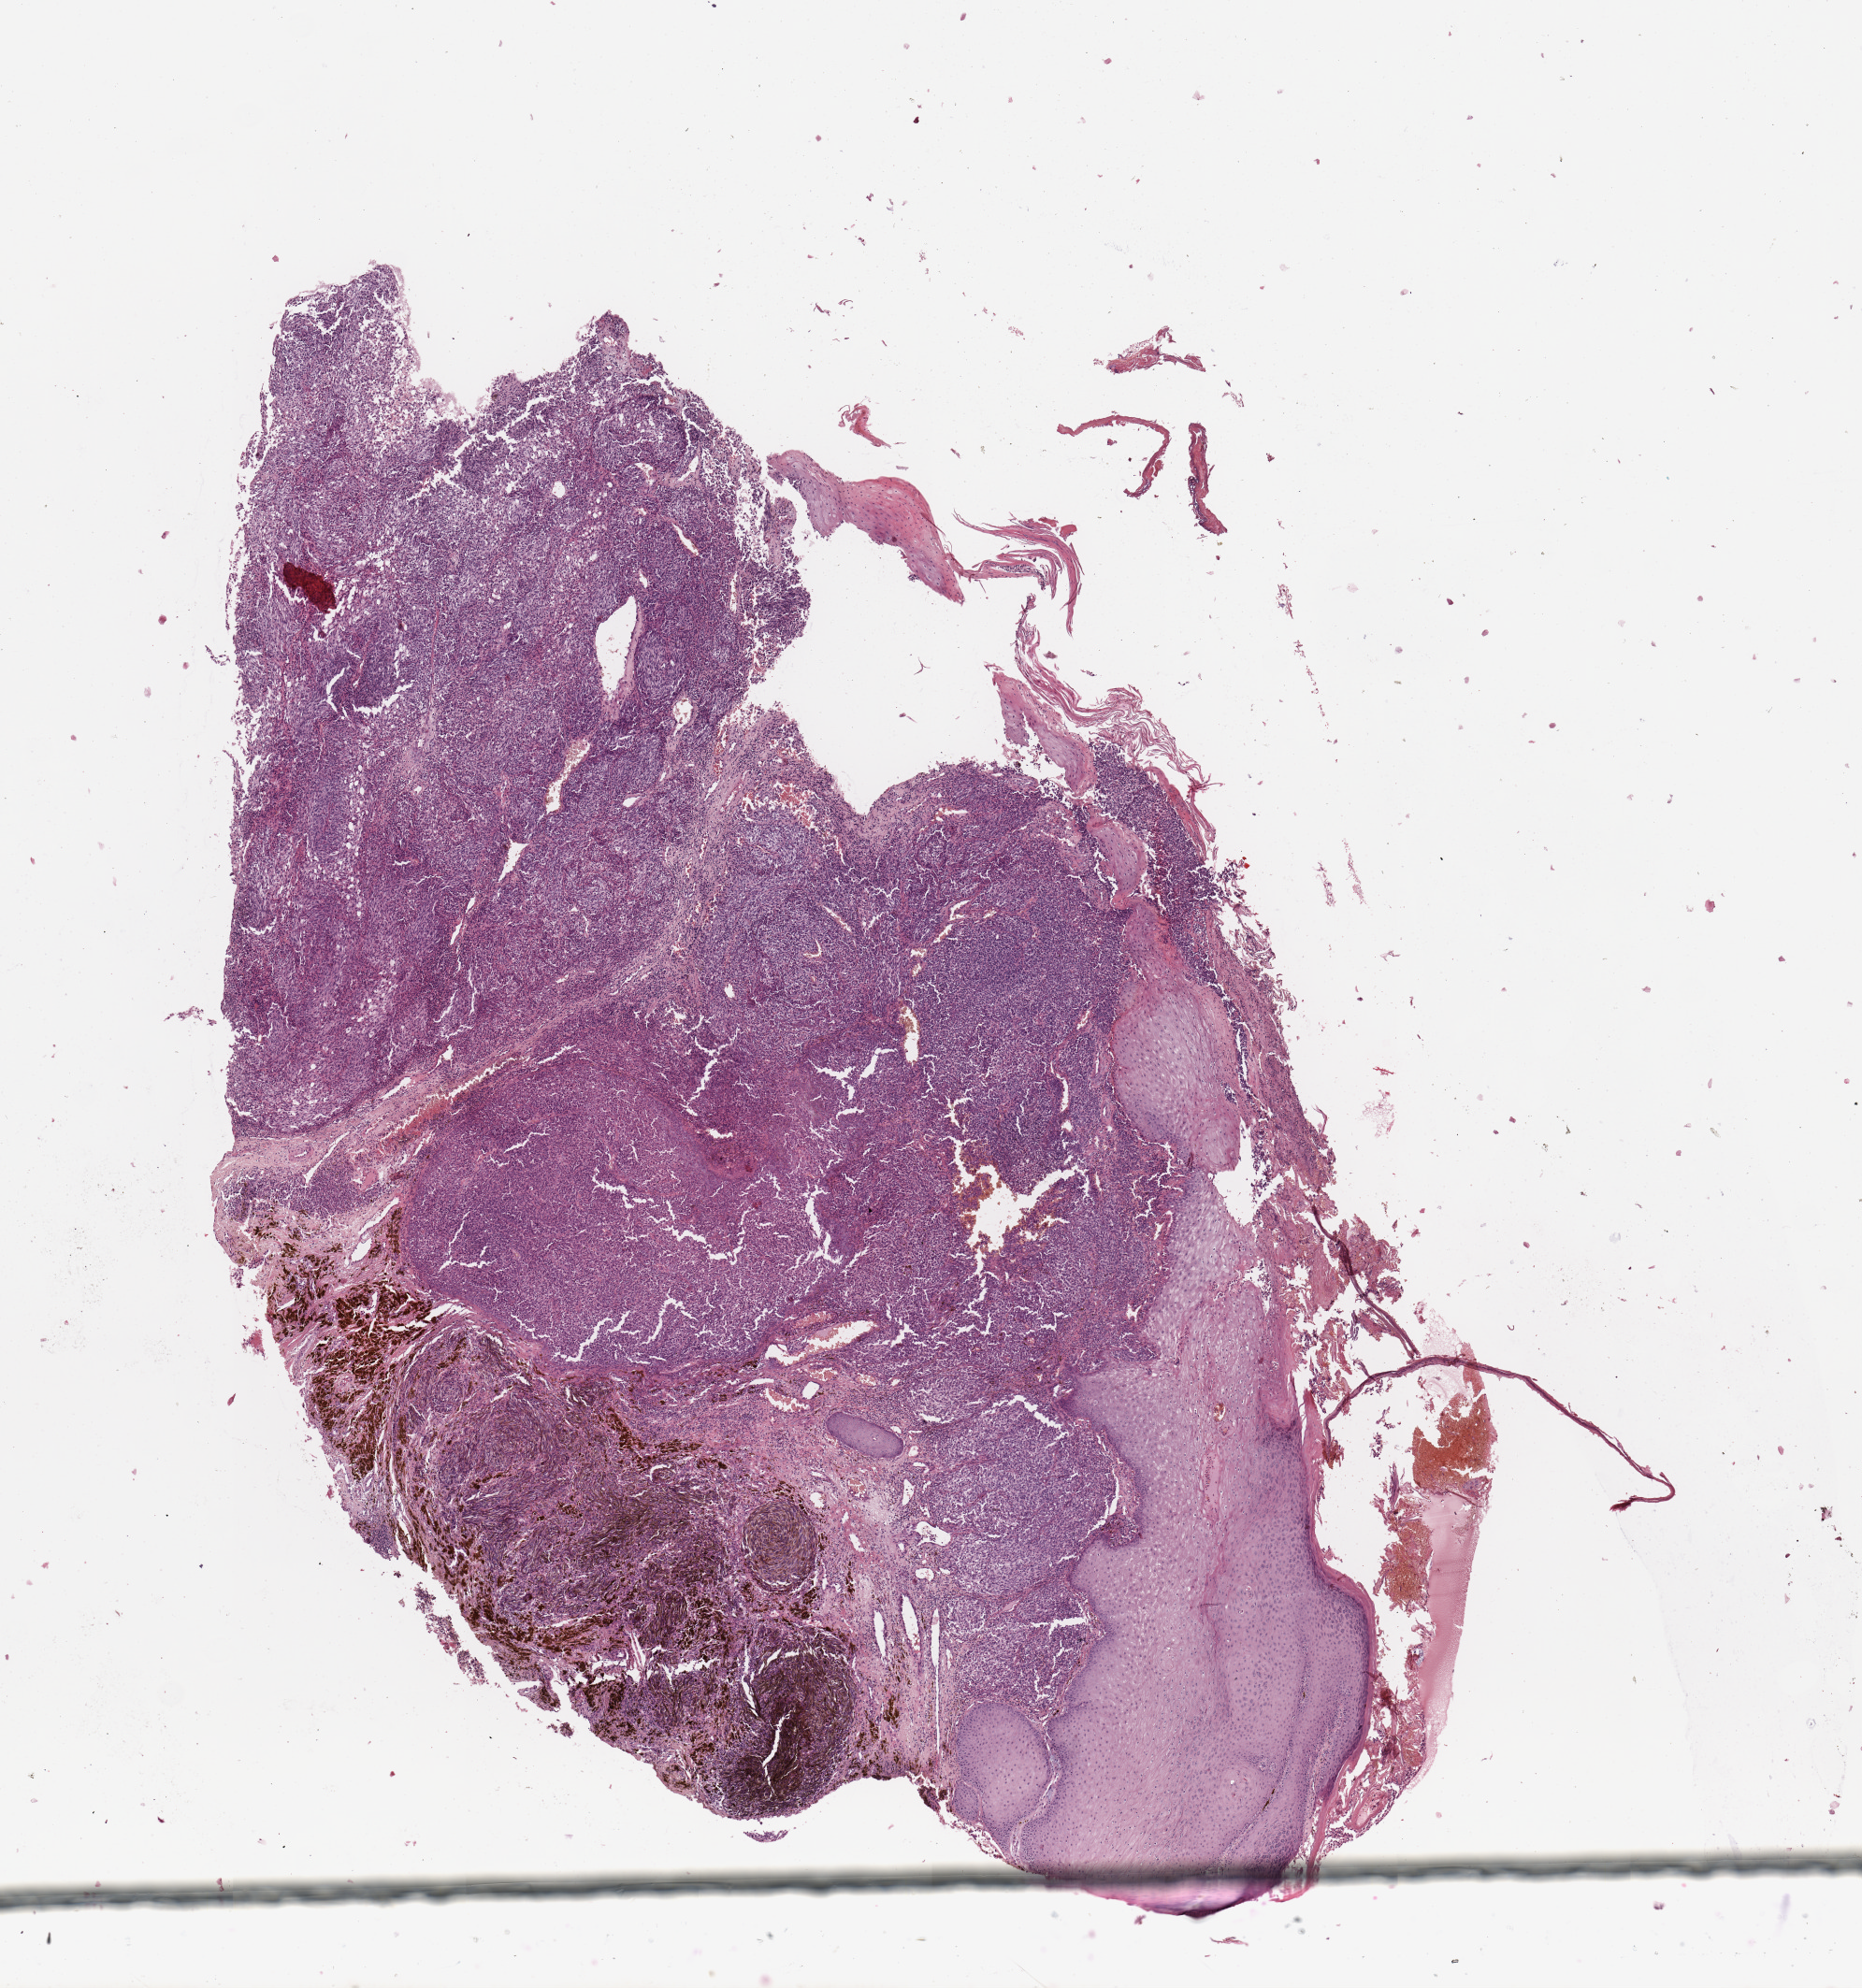
Digitized Hematoxylin and eosin (H&E) stained tissue section (whole slide), low-resolution overview of the scanned area, about 7.9 x 8.4 mm (from a 20x scan); melanoma tumour tissue; sampled site not recorded. 73-year-old male patient.
Primary tumour site (as recorded): trunk. AJCC pathologic stage: IIC. Diagnosis: Malignant melanoma, NOS.